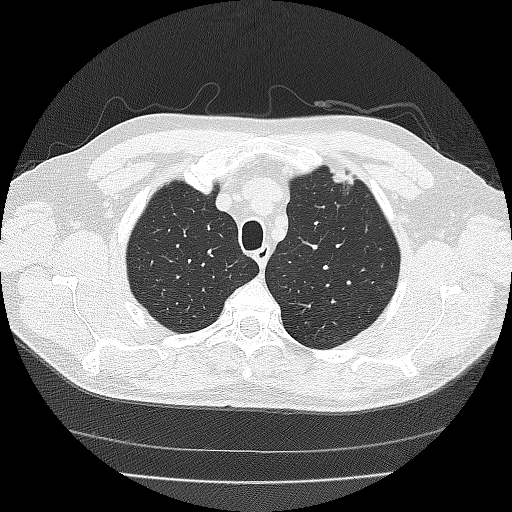
Low-dose screening chest CT, axial slice. Third screening round (two years after baseline). Lung window (W 1500 / L -600 HU). 2 mm slice thickness. Reconstruction kernel FC30 (as recorded). Slice 34 of 167 in the series. Male participant, aged 56 years at enrolment.
Expert reader's lesion annotation, bounding box [x1, y1, x2, y2] px = [323, 159, 366, 198]. The exam's reader record, not a measurement of the box and not confirmed to be the same lesion: non-calcified nodule or mass ≥4 mm, left upper lobe, 18 × 10 mm, spiculated (stellate) margins, soft tissue attenuation, pre-existing on the prior screen: yes; interval growth: yes. Official screen result: positive, other.